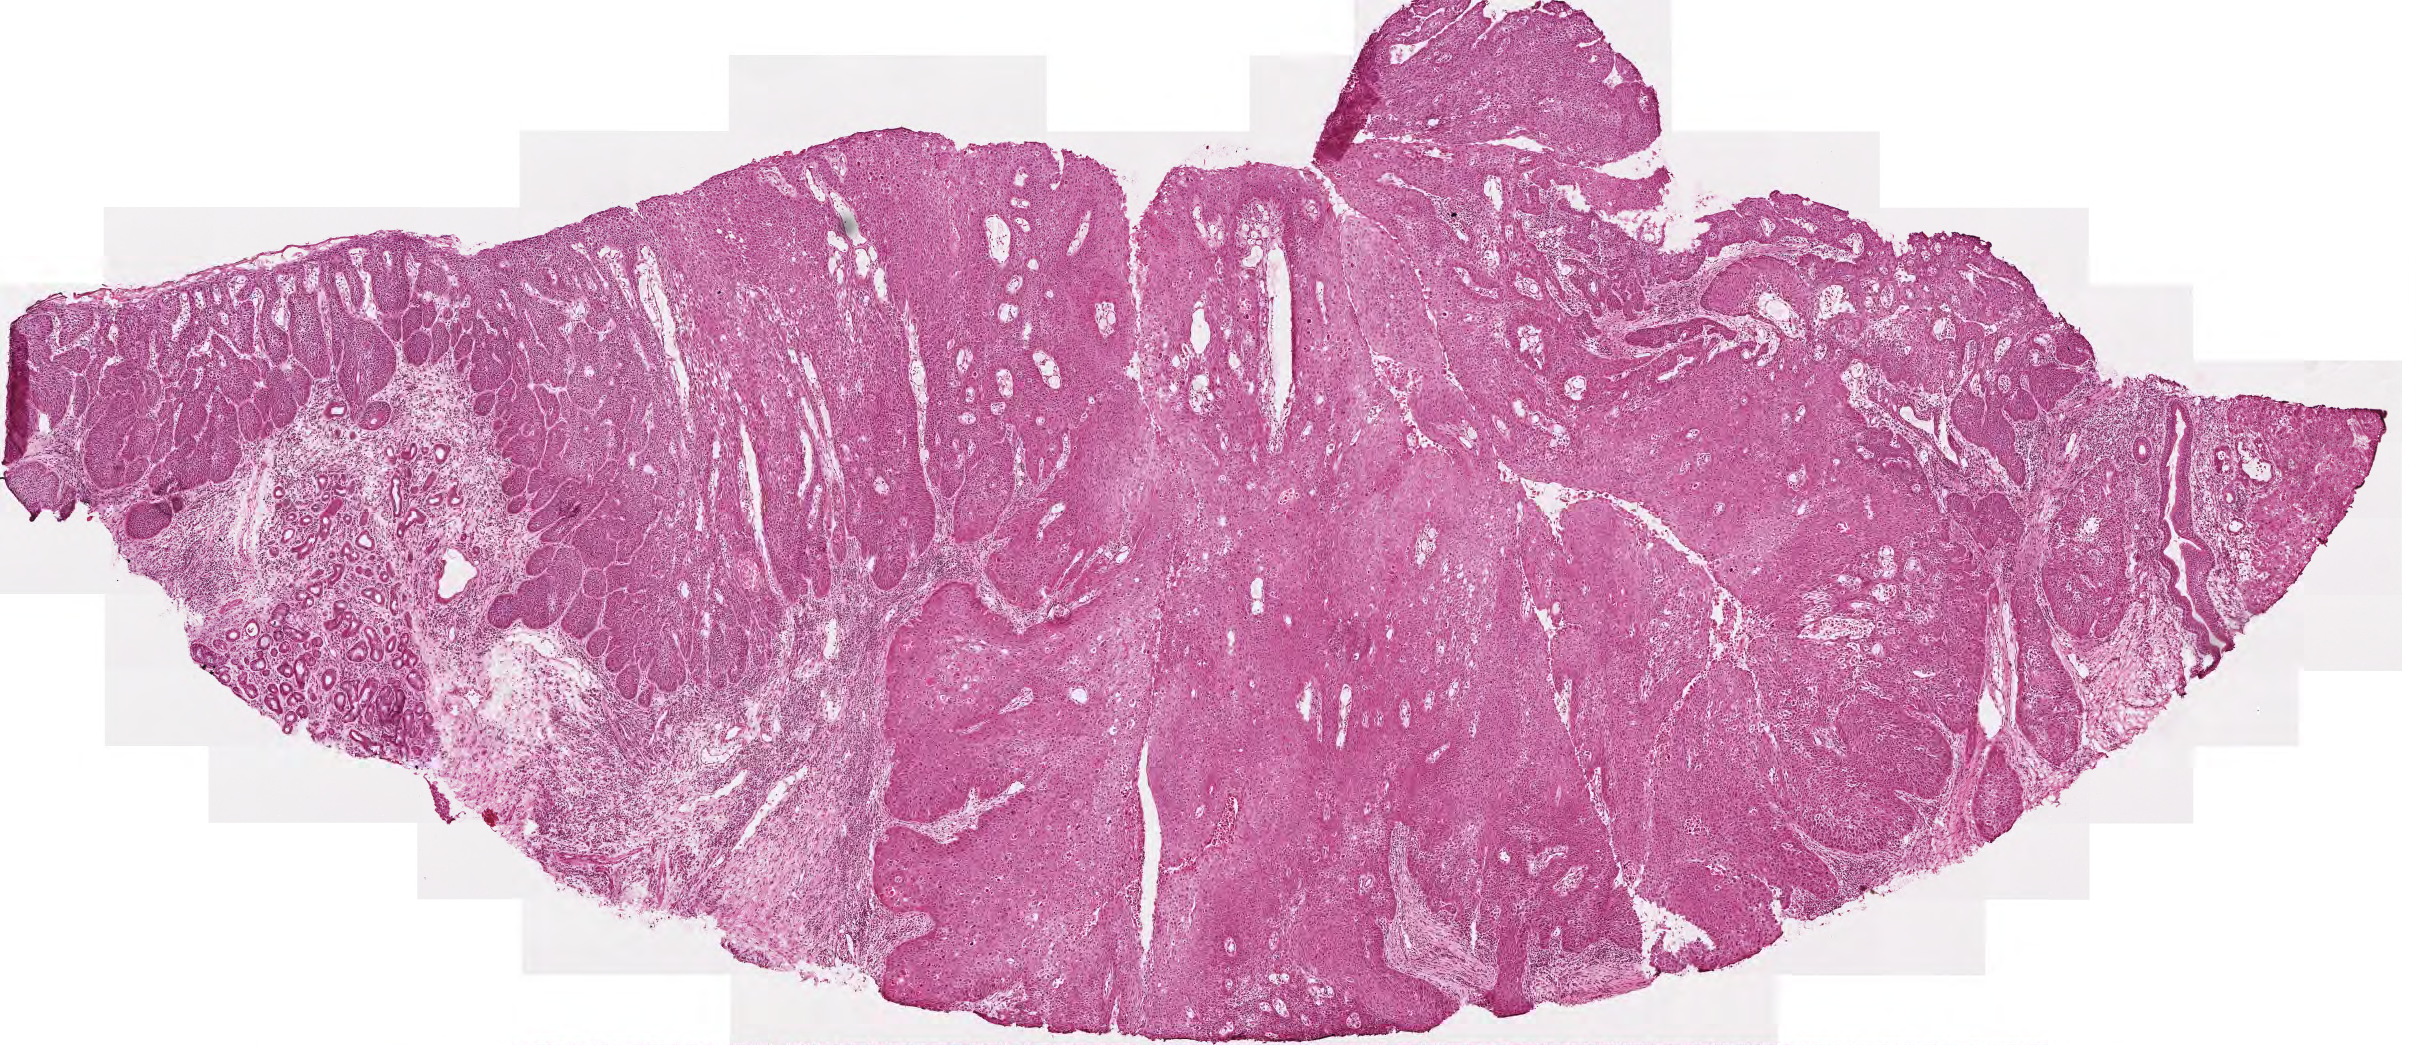
H&E whole-slide image, low-resolution overview of the scanned area, about 4.8 x 2.1 mm; frozen section; primary tumour sample from the head and neck. Male patient; age at initial diagnosis 54 years. Histologic grade: G2 (moderately differentiated). Slide review estimates, as recorded: tumour cells 75%, tumour nuclei 75%, normal cells 10%, stromal cells 15%, necrosis 0%.
Pathologic diagnosis: Squamous cell carcinoma, NOS (overlapping lesion of lip, oral cavity and pharynx). AJCC pathologic stage: IVA (6th edition).